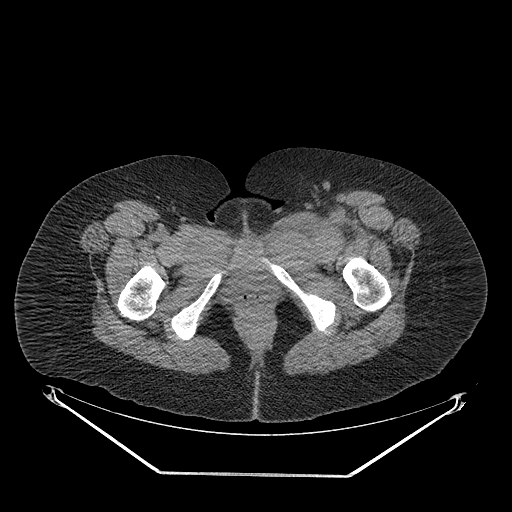
CT of an extremity soft-tissue mass (from a PET/CT study), one axial slice. Slice 47 of 267 in the series (ordered by position). Reconstruction kernel STANDARD. 140 kVp. Soft-tissue window (W 400 / L 40 HU). 3.75 mm slice thickness. 512 × 512 image matrix, field of view 500 × 500 mm. Female patient. Case-level facts recorded for this patient, not image findings: histological type: myxofibrosarcoma; grade: intermediate; site of the primary tumour: left thigh.
Outlined on this slice (expert contour drawn on MRI and transferred to this co-registered scan by the dataset authors):
- gross tumour volume including surrounding oedema: bounding box (x1, y1, x2, y2) in pixels: (263, 206, 364, 250)